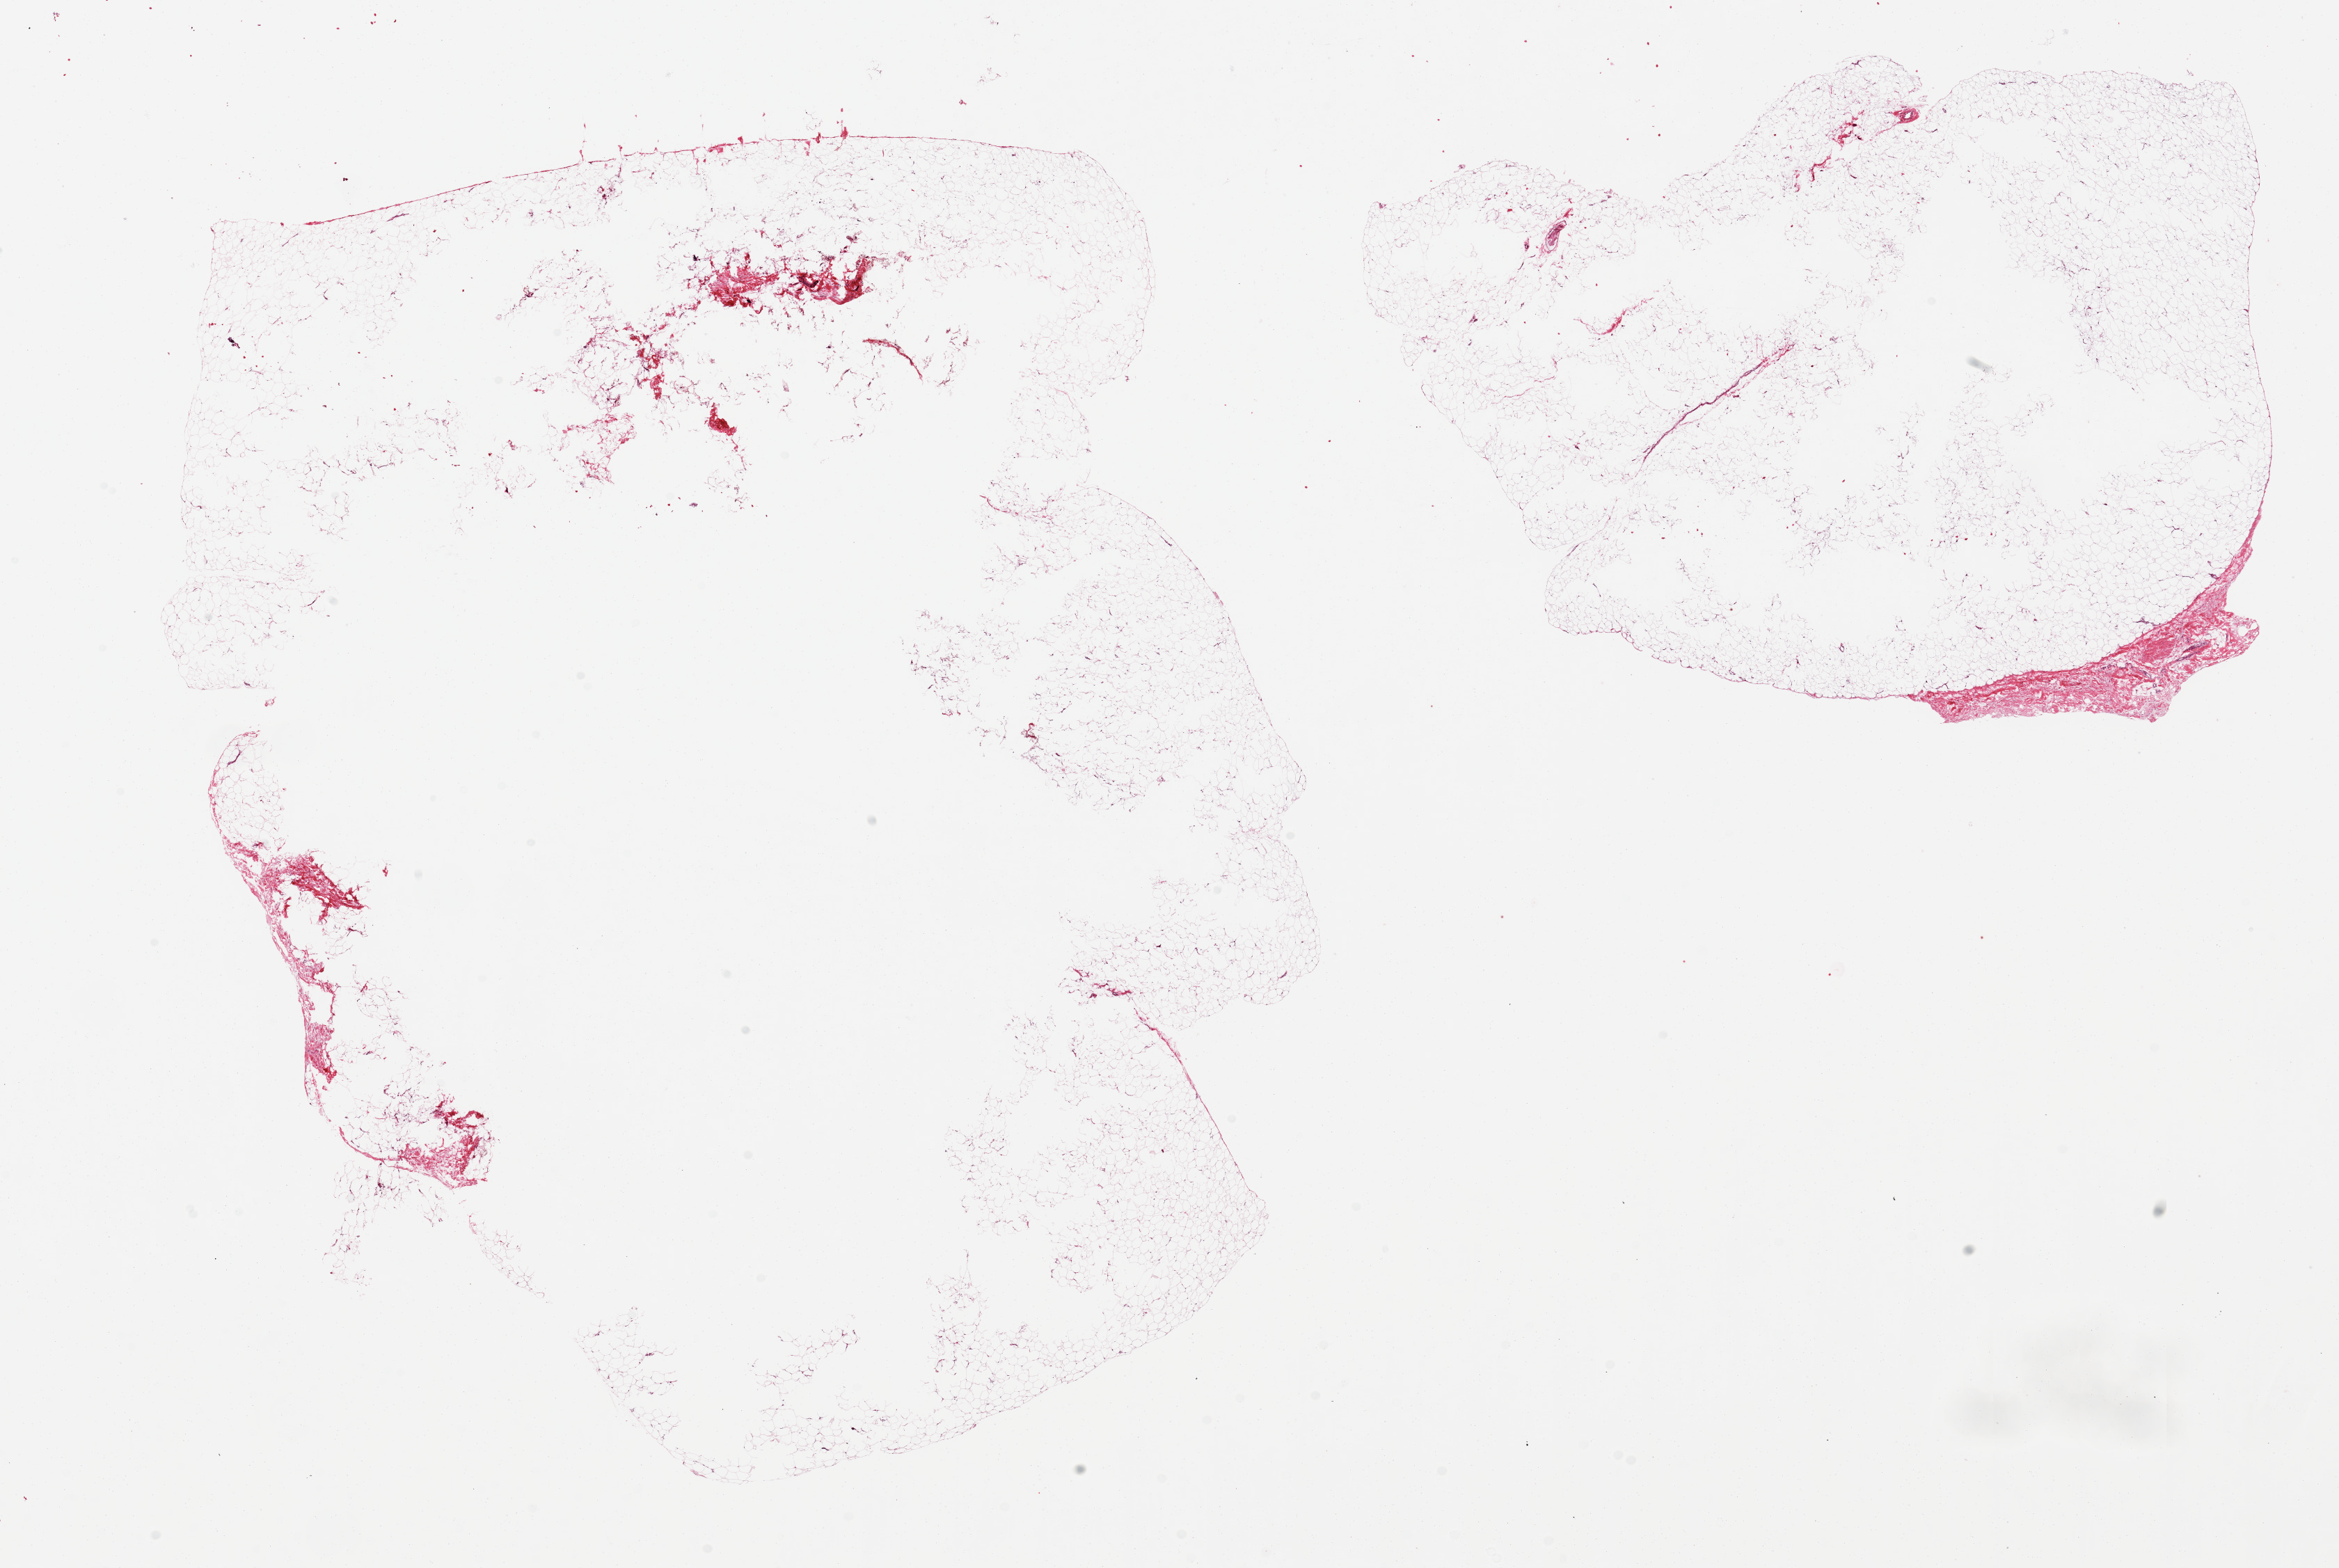
Whole-slide image, H&E stain, brightfield — shown as a low-resolution overview of the whole scanned area (about 26.6 x 17.8 mm, acquisition: 20x scan), PAXgene-fixed, paraffin-embedded tissue, target tissue: adipose tissue, tissue donor sample. Female donor.
- reviewer comment on this tissue sample: 2 pieces, 15x12 & 10x8 mm; large central defects especially in larger piece